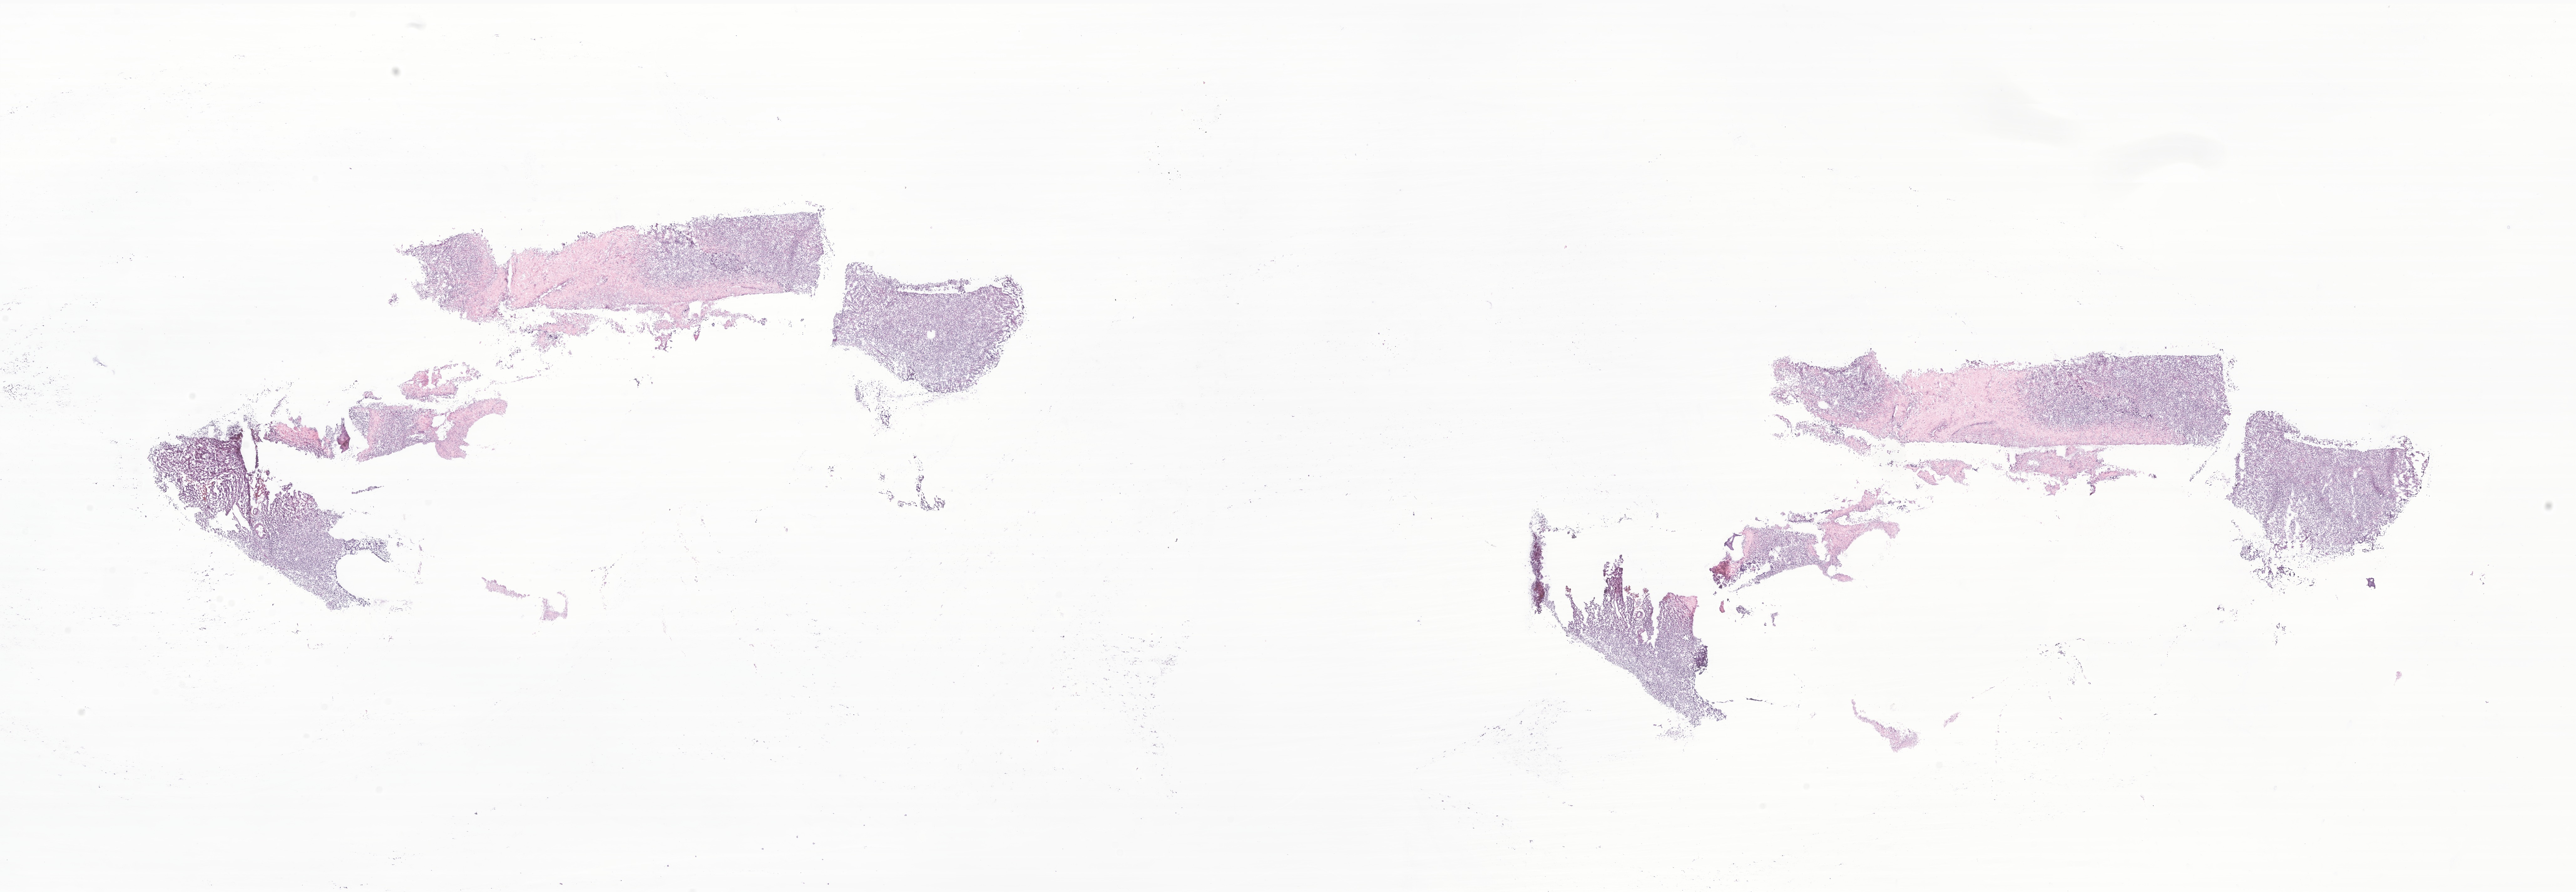
Digitized haematoxylin and eosin-stained section of tumor tissue from the brain stem, a low-resolution overview of the entire scanned area, about 34.7 x 12.0 mm, frozen section (OCT-embedded). Patient male; age 149 months.
Recorded diagnosis: Medulloblastoma, NOS.